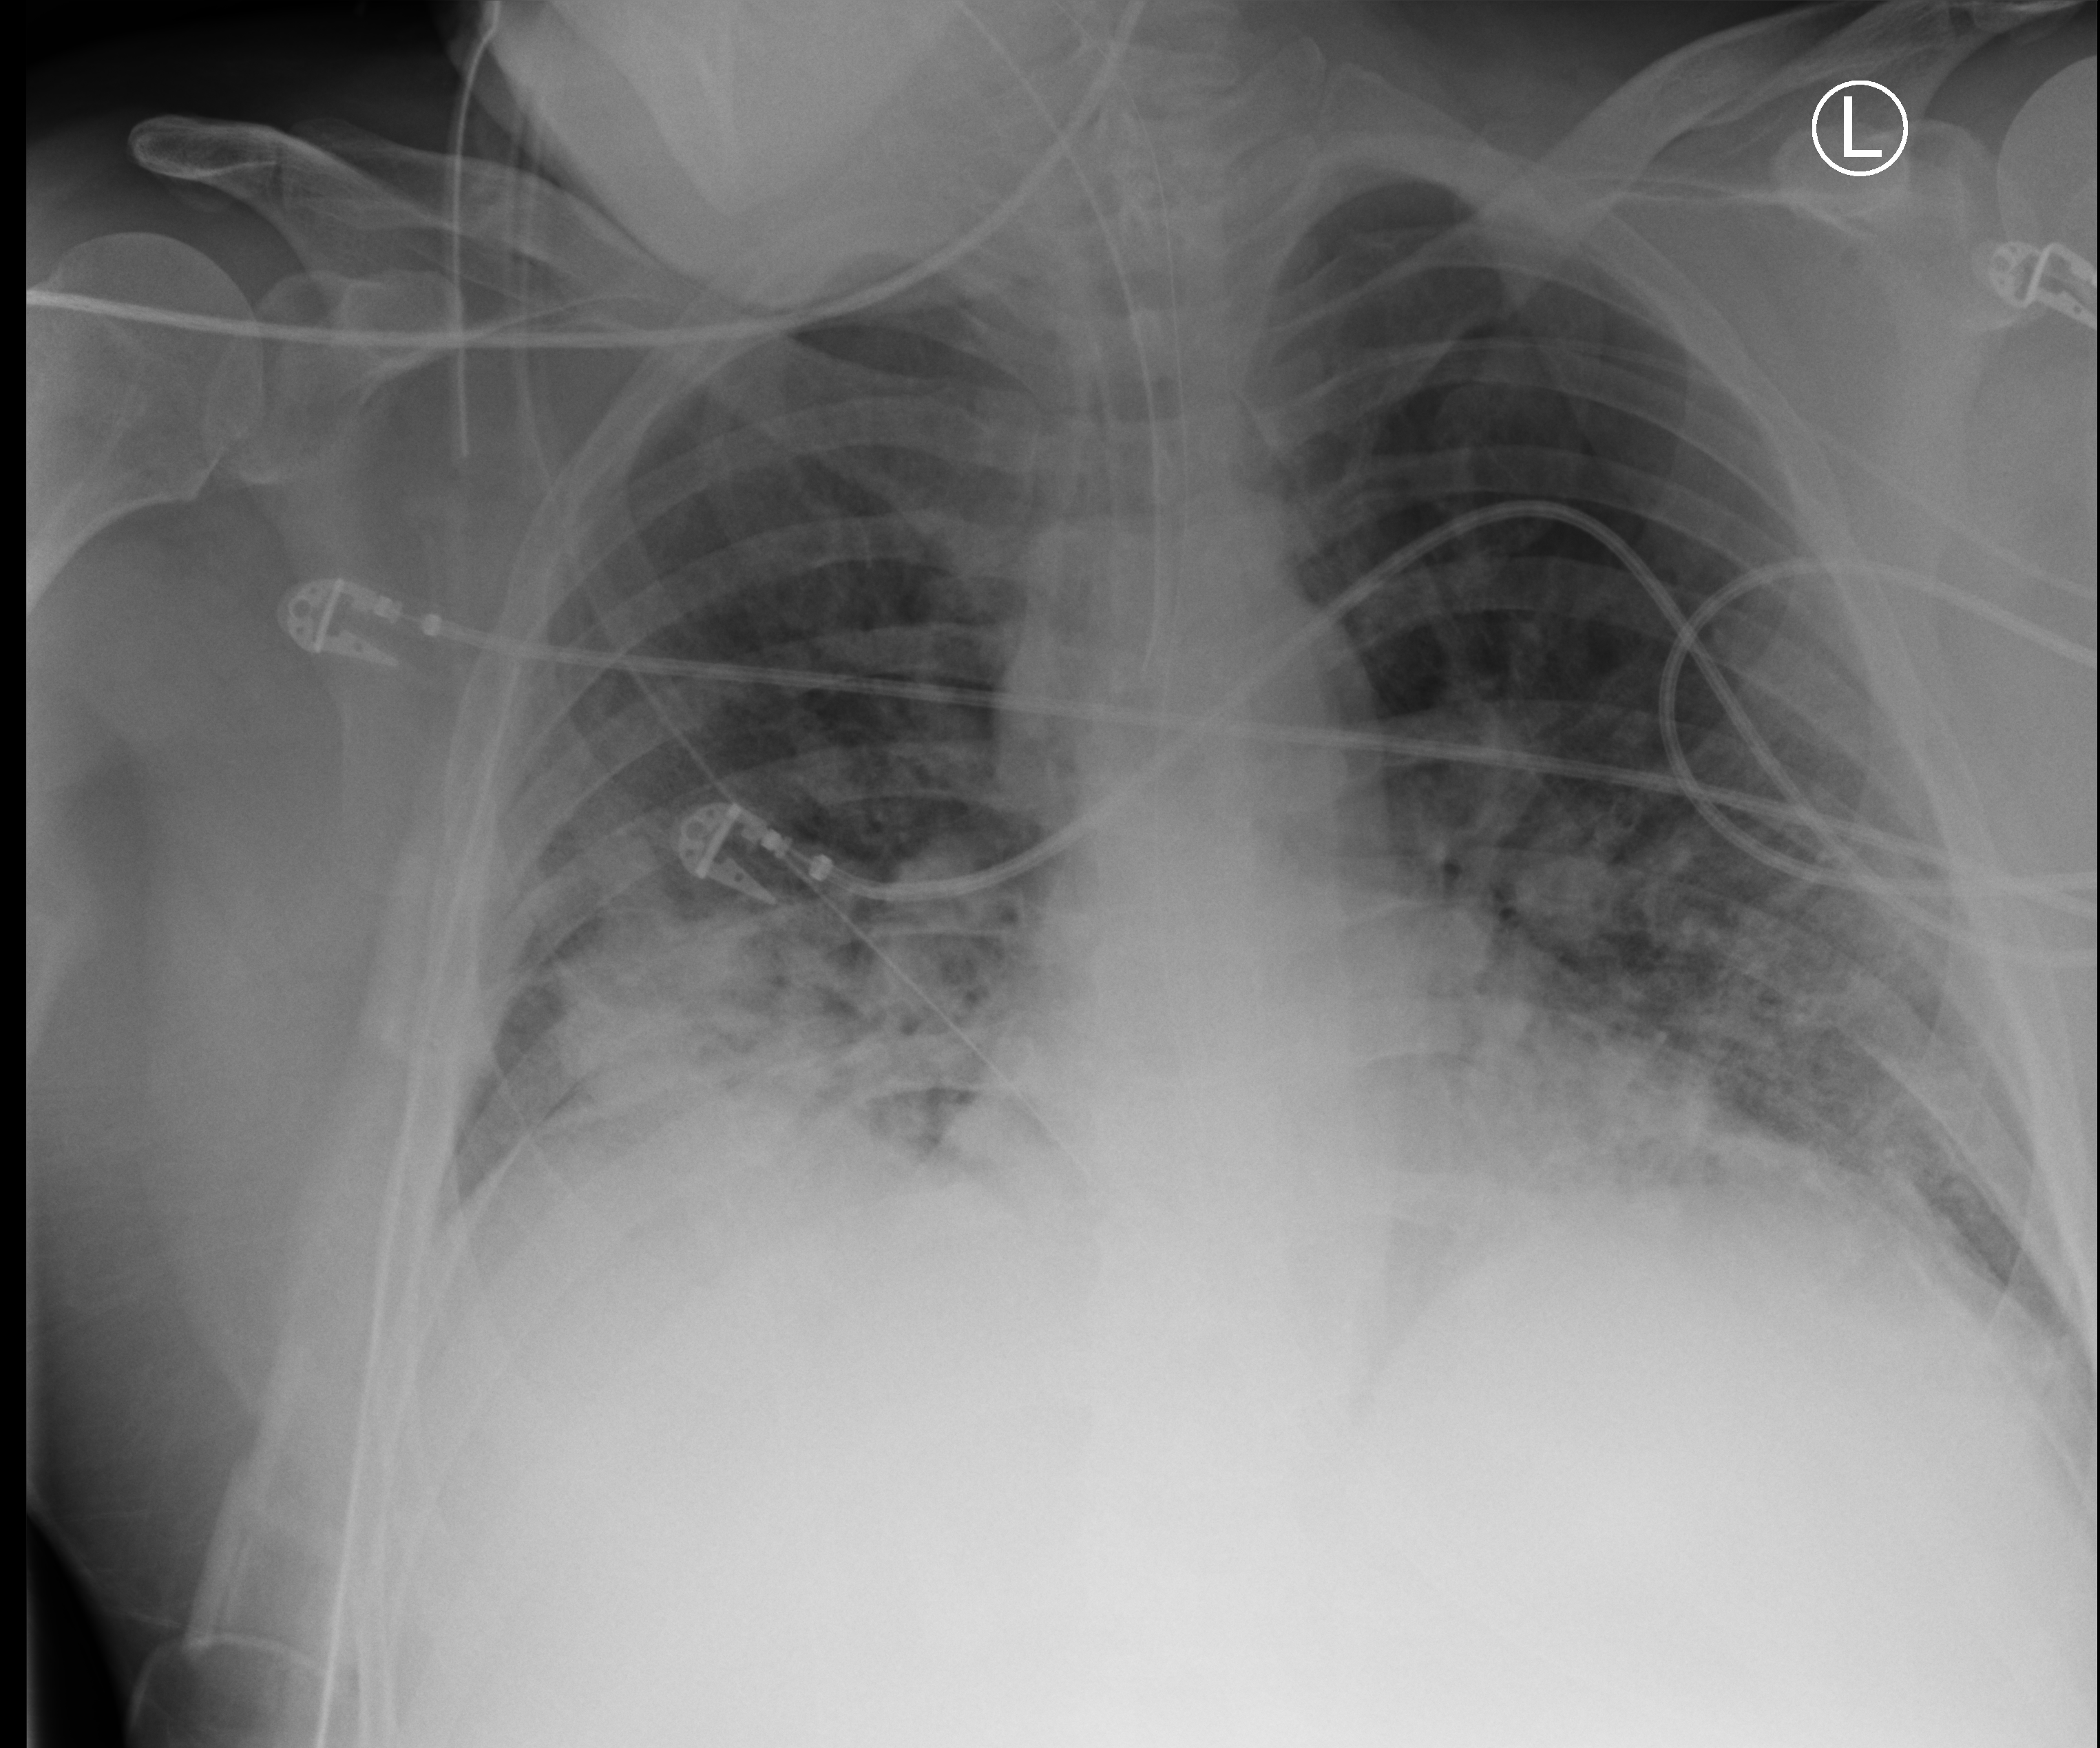
Bedside chest radiograph (computed radiography). Patient hospitalised with COVID-19; male, aged 18–59 years.
Hospital-stay facts (about this admission, not read from this image; timing relative to this image not recorded): mechanically ventilated during this hospital stay: yes; admitted to intensive care during this hospital stay: yes; length of hospital stay: 80 days.